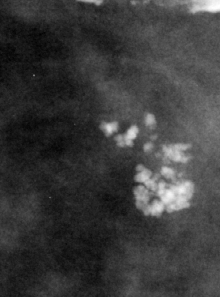
Region of interest cut from a scanned film mammogram (one marked finding); right breast; CC view; BI-RADS breast density category 2 (scale 1–4).
- Marked abnormality: calcifications, morphology pleomorphic, distribution clustered; BI-RADS assessment category 4; pathology (as recorded): benign.